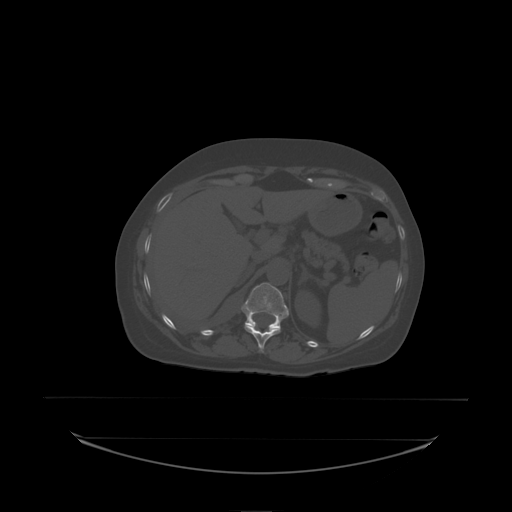
CT including the spine, one axial slice; slice 99 of 242 in the series (ordered by position); bone window (W 1800 / L 400 HU); 512 × 512 image matrix, field of view 500 × 500 mm. Female patient, age 53 years. Case-level facts recorded for this patient, not image findings: primary cancer: lung; vertebrae with lytic lesions (as recorded): T7, L1.
Annotated regions visible in this slice (semi-automatically segmented with operator editing):
- T11 vertebra: bounding box [x1, y1, x2, y2] px = [245, 326, 281, 338]
- T12 vertebra: [241, 283, 290, 330]